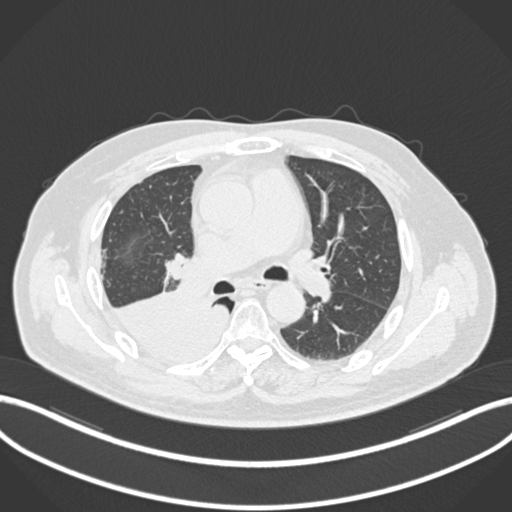
Chest CT, one axial slice. Slice 113 of 218 in the series (ordered by position). Reconstruction kernel B30f. 120 kVp. Lung window (W 1500 / L -600 HU). 512 × 512 image matrix. Patient: male, 68 years. Case-level facts recorded for this patient, not image findings: clinical TNM (as recorded): T2a N0 M0.
Annotated regions visible in this slice (bounding box drawn by a radiologist):
- lung tumour (recorded histology: adenocarcinoma): bounding box [x1, y1, x2, y2] px = [111, 288, 234, 375]